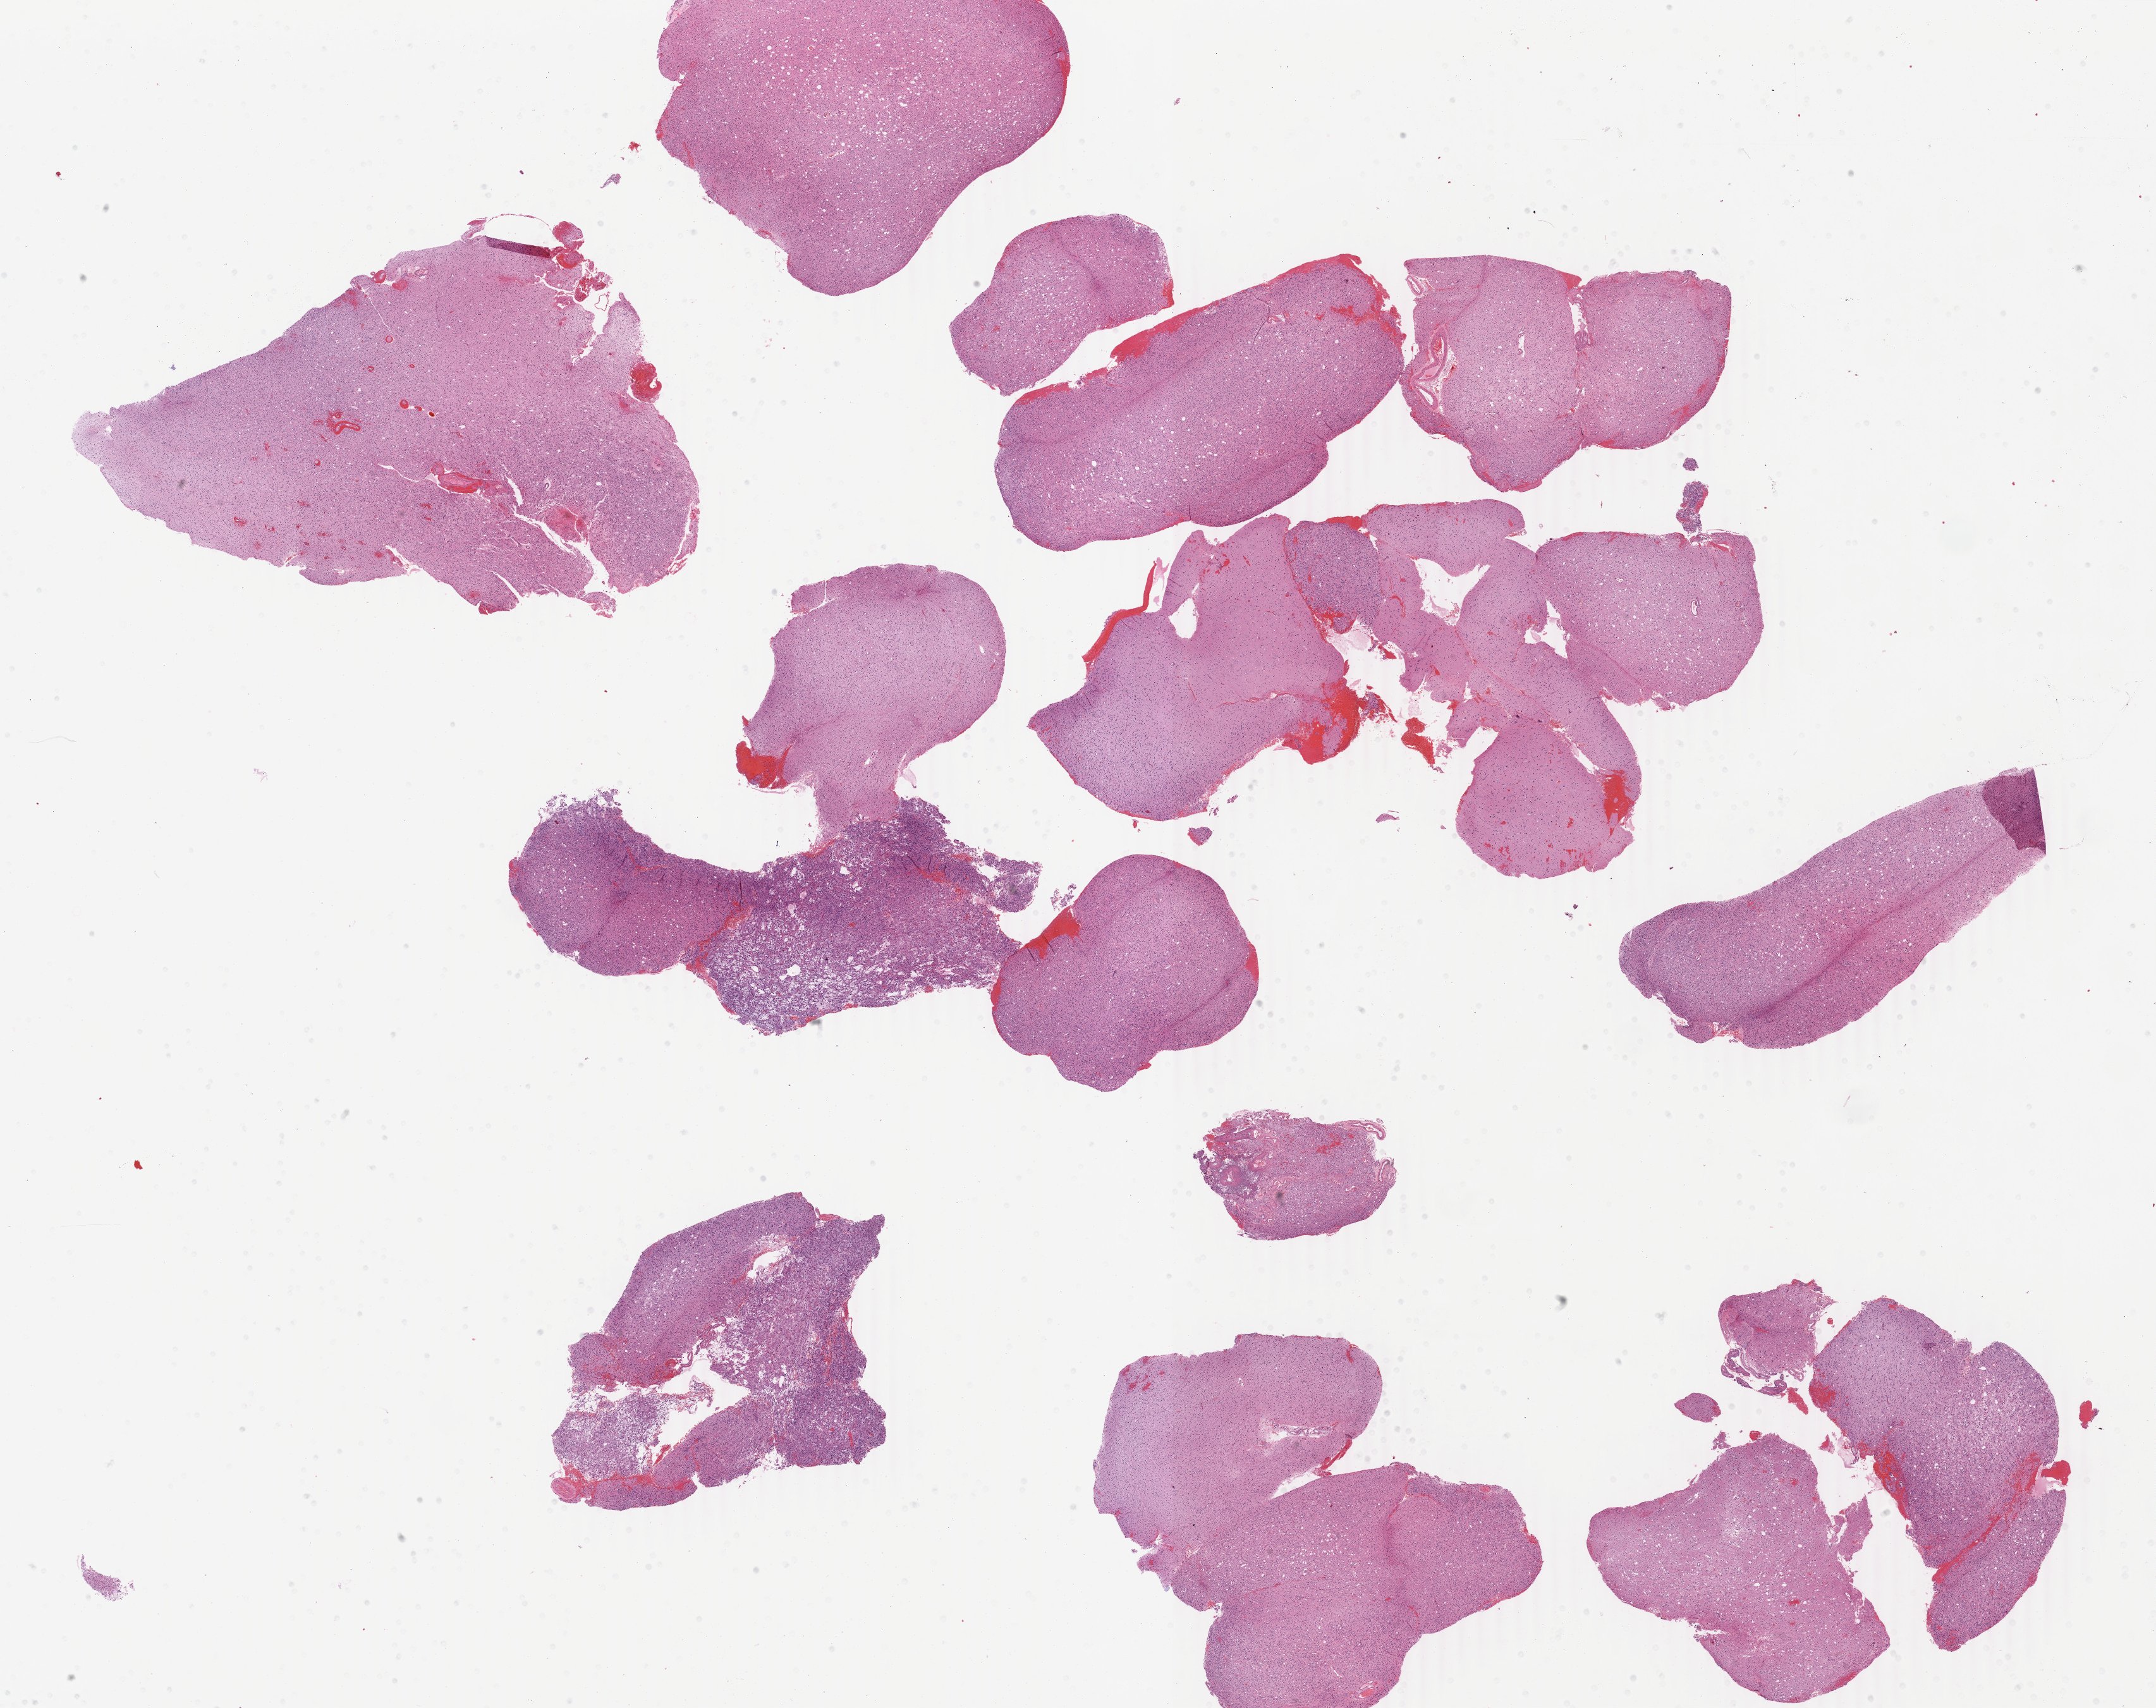
Hematoxylin and eosin (H&E) stained whole-slide image, low-resolution overview of the scanned area, about 27.1 x 21.5 mm (slide scanned at 40x), FFPE section, primary tumour sample from the brain. Male, age 43 years at initial diagnosis. Histologic grade: G3 (poorly differentiated).
• laterality: right
• pathologic diagnosis: Astrocytoma, anaplastic